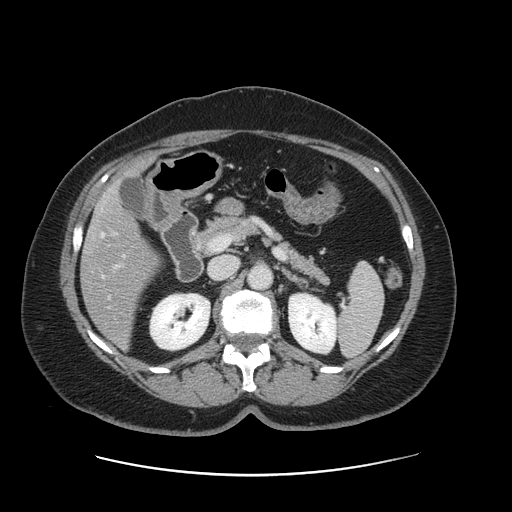
Contrast-enhanced abdominal CT, one axial slice. Position 71 of 161 along the scan axis. 120 kVp. Intravenous contrast given. Soft-tissue window (W 400 / L 40 HU). 512 × 512 image matrix. Female patient, age 62 years. Case-level facts recorded for this patient, not image findings: diagnosis: colorectal cancer liver metastases, imaged before liver resection; multiple liver metastases: no; largest metastasis: 2.5 cm.
Structures marked on this image (manually delineated by an expert):
- hepatic veins: bounding box <102,233,110,299> (left, top, right, bottom; pixels)
- liver: <82,187,161,348>
- portal vein (with intrahepatic branches): <112,232,118,267>